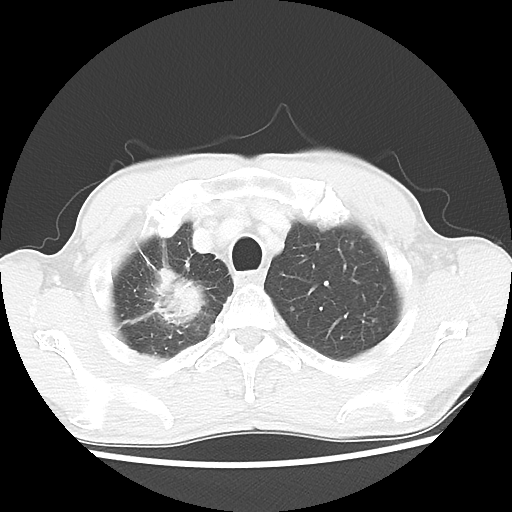
Chest CT, one axial slice. Reconstruction kernel LUNG. 100 kVp. Lung window (W 1500 / L -600 HU). 5 mm slice thickness. 512 × 512 image matrix, field of view 323 × 323 mm. Male patient, age 66 years. From the clinical record (not read from this slice): clinical TNM (as recorded): T2 N0 M1a.
Annotated regions visible in this slice (bounding box drawn by a radiologist):
- lung tumour (recorded histology: adenocarcinoma): bounding box [x1, y1, x2, y2] px = [140, 266, 208, 328]